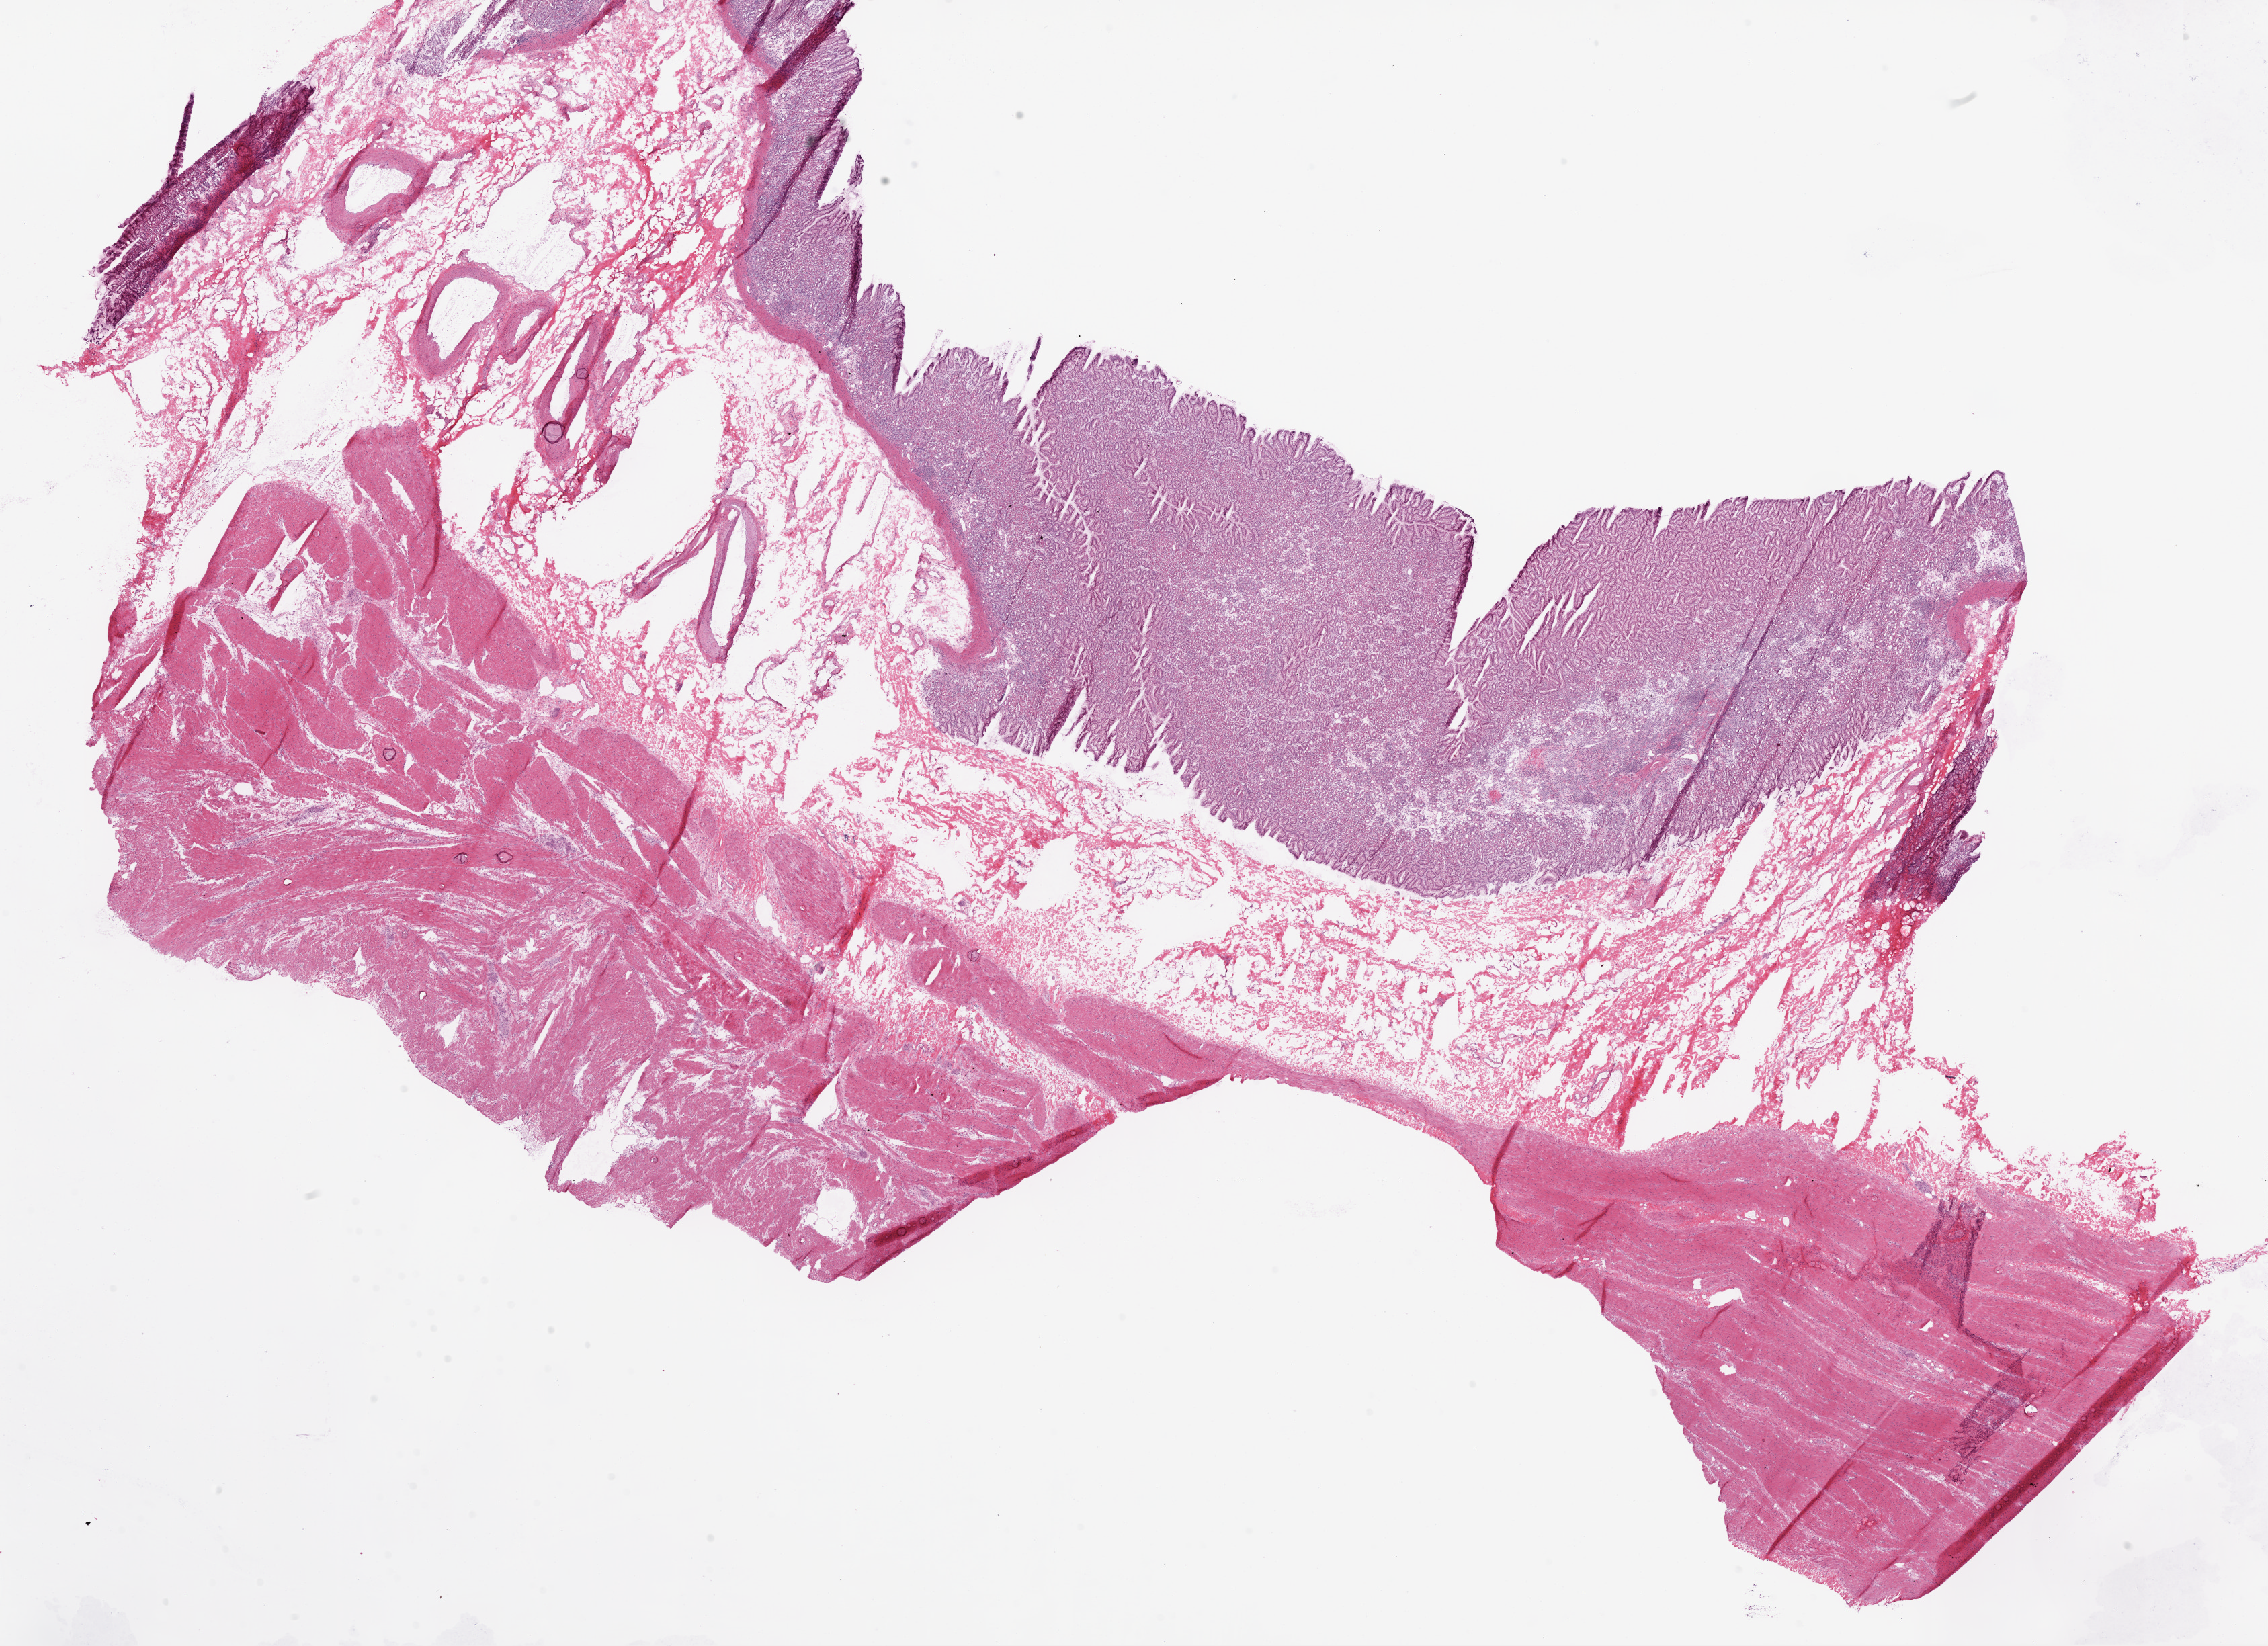
Digitized H&E tissue section (whole slide) — shown as a low-resolution overview of the whole scanned area (about 27.1 x 19.7 mm), frozen section from the bottom of the tissue portion, stomach, solid tissue normal (non-tumour tissue) sample. Male patient; age at initial diagnosis 80 years.
This section: solid tissue normal sample (biorepository sample class). Patient diagnosis: Adenocarcinoma, NOS (gastric antrum).